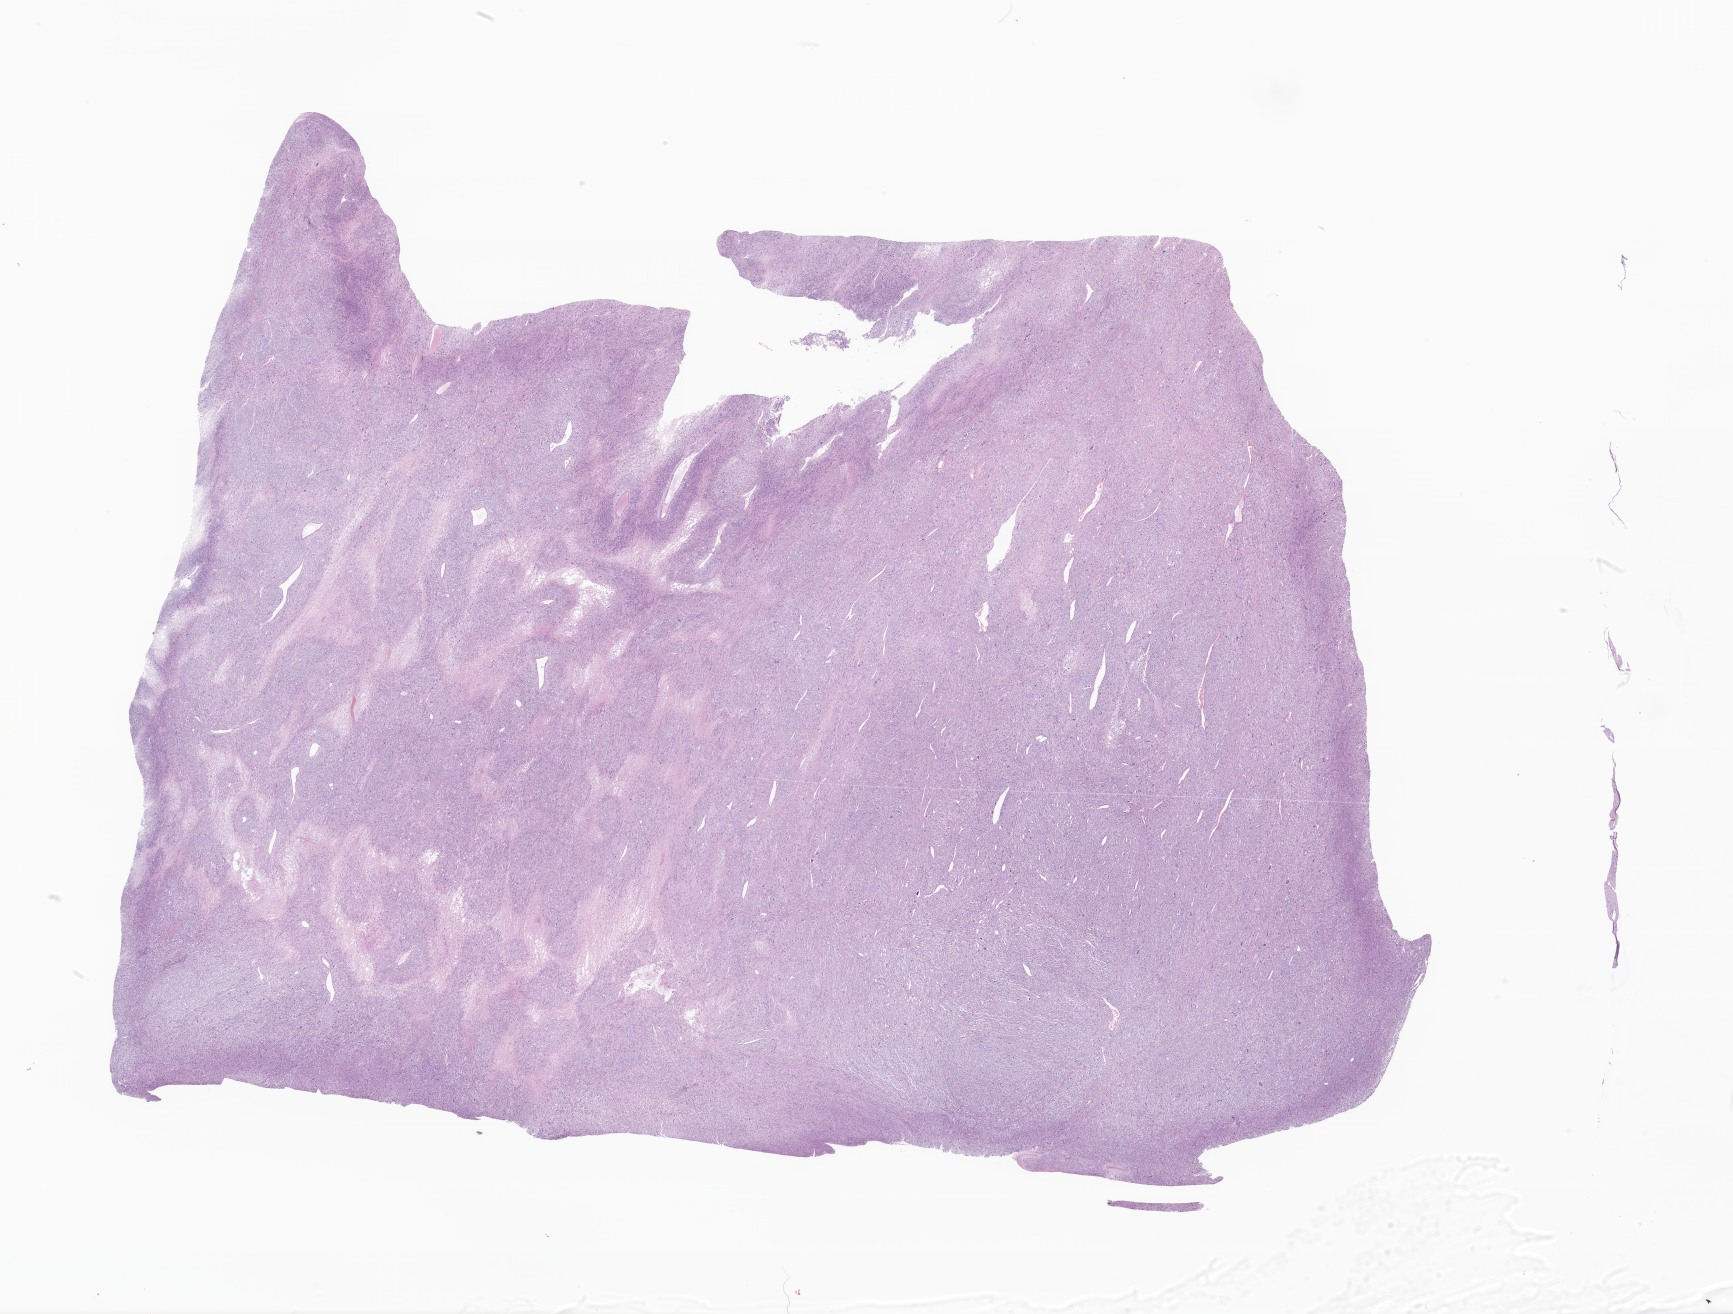
H&E whole-slide image of tumor tissue from the kidney — low-resolution overview of the scanned area, about 29.2 x 22.2 mm; formalin-fixed paraffin-embedded section. Patient: female, age 51 months.
Diagnosis (ICD-O-3 morphology term): Nephroblastoma, NOS.